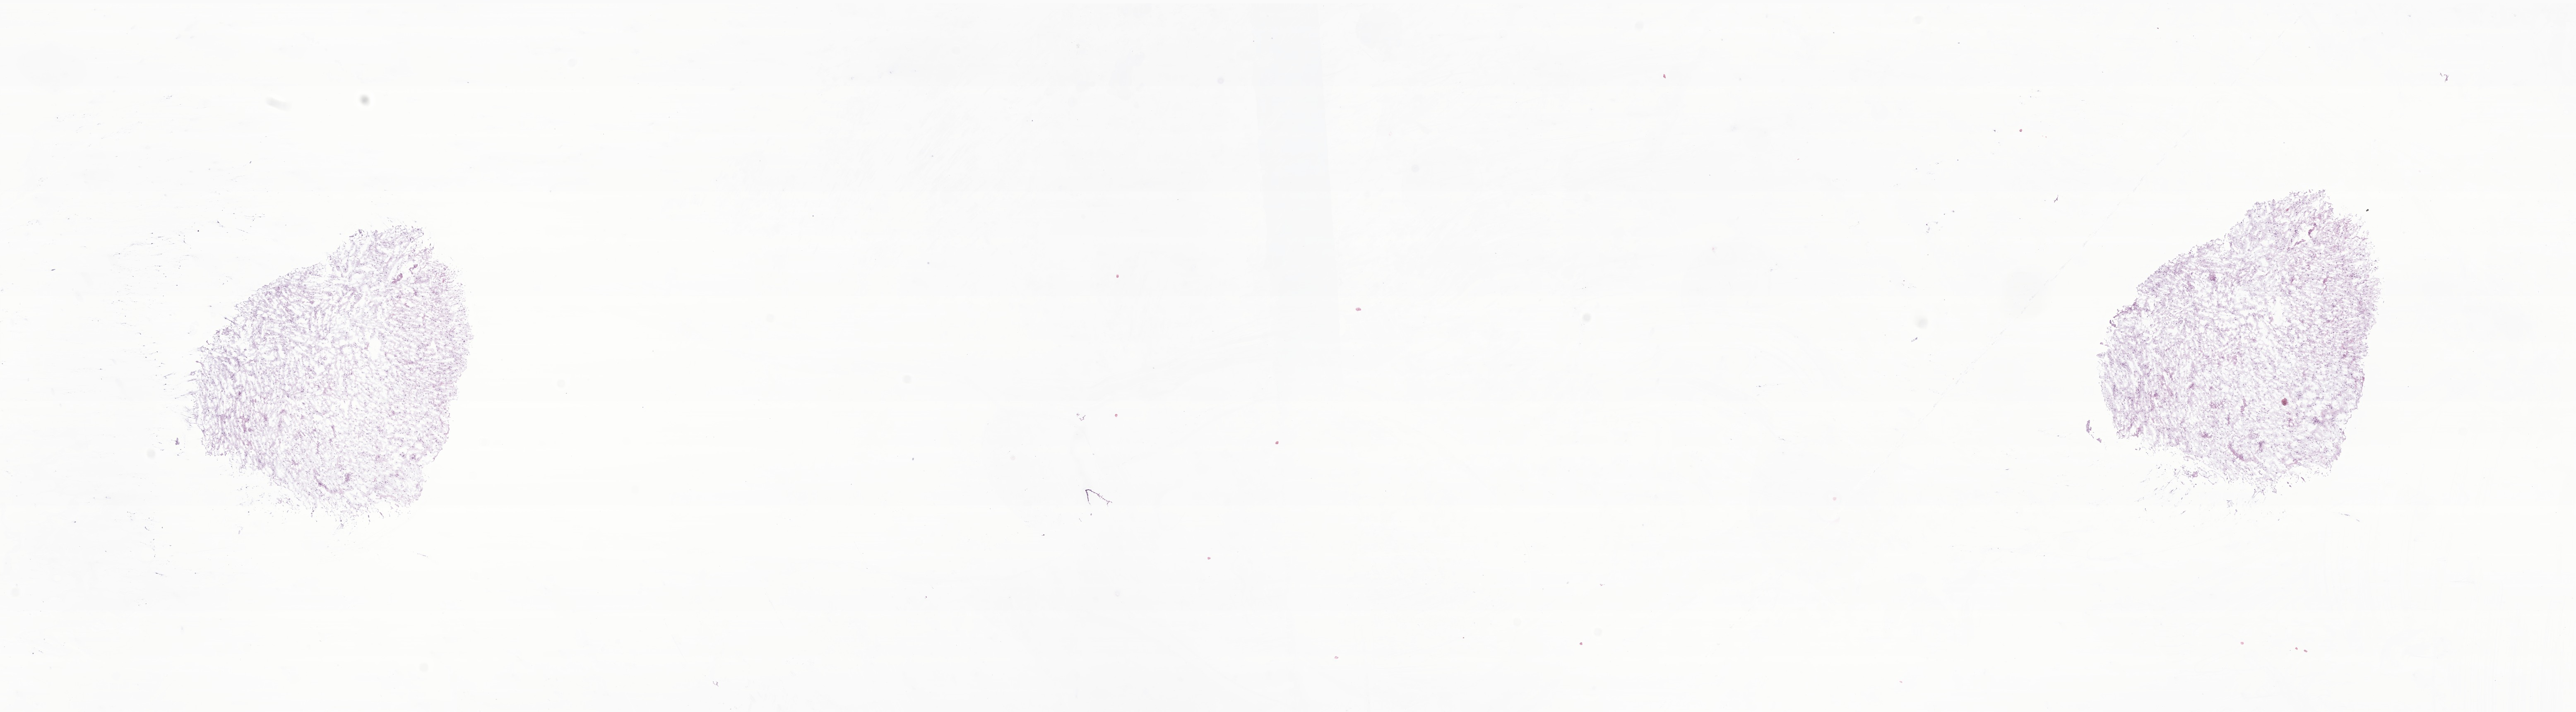
Haematoxylin and eosin whole-slide image of tumor tissue from the brain — a low-resolution overview of the entire scanned area, about 26.2 x 7.3 mm, frozen section (OCT-embedded). Female patient, age 134 months (11 years 2 months).
Diagnosis (ICD-O-3 morphology term): Pilocytic astrocytoma.